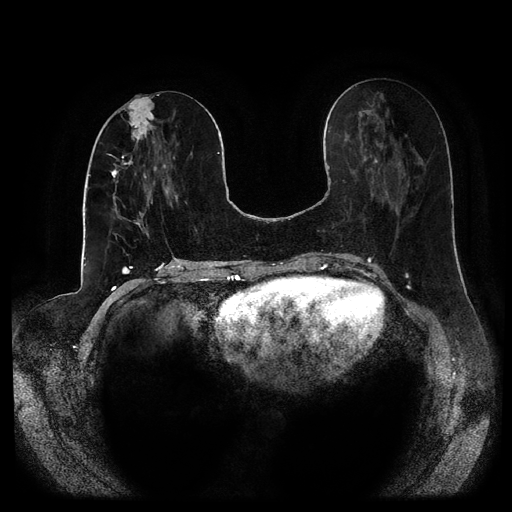
Breast MRI (dynamic contrast-enhanced, multi-phase), one axial slice. Slice 40 of 116 in the series (ordered by position). Dynamic contrast-enhanced series, time point 2 of 5 at this slice position (early post-contrast). 1.5 T. TE 2.6 ms, TR 5.2 ms. 2 mm slice thickness. 512 × 512 image matrix, field of view 380 × 380 mm. Female patient, age 53 years.
Structures marked on this image (semi-automatic segmentation, software-assisted and operator-edited):
- breast lesion (labelled 'tumour' in the annotation; benign lesions carry a separate 'benign' label): bounding box [x1, y1, x2, y2] px = [124, 96, 156, 149]
- breast lesion (labelled 'tumour' in the annotation; benign lesions carry a separate 'benign' label): [110, 168, 120, 180]